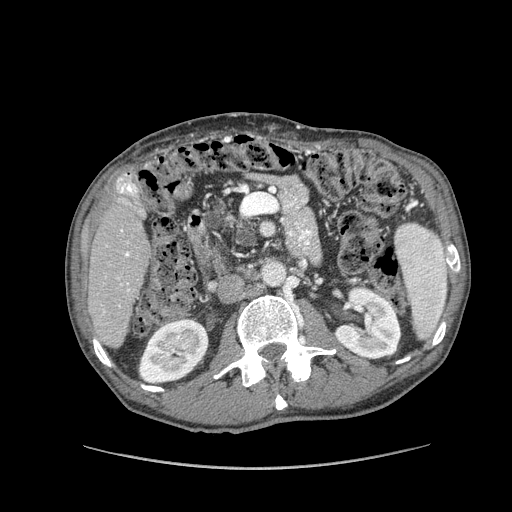
Contrast-enhanced abdominal CT (liver protocol), one axial slice. Position 35 of 162 along the scan axis. Reconstruction kernel STANDARD. 100 kVp. Soft-tissue window (W 400 / L 40 HU). 2.5 mm slice thickness. 512 × 512 image matrix, field of view 400 × 400 mm. Case-level facts recorded for this patient, not image findings: diagnosis: hepatocellular carcinoma (patient treated with transarterial chemoembolisation; whether this scan precedes or follows treatment is not stated here); TNM stage (as recorded): Stage-IIIA; Child-Pugh class: A; tumour nodularity: multinodular; tumour size: 9.9 cm.
Annotated regions visible in this slice (semi-automatic segmentation, software-assisted and operator-edited):
- liver parenchyma outside the tumour (the mass and vessels are separate outlines, so this box may not span the whole liver): bounding box (x1, y1, x2, y2) in pixels: (88, 174, 150, 347)
- liver vessels: (117, 178, 137, 291)